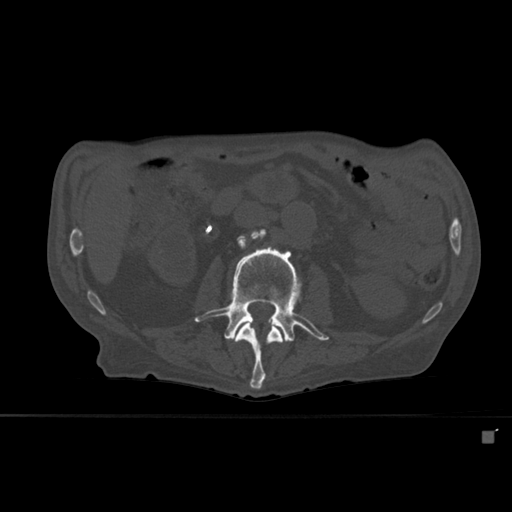
CT including the spine, one axial slice. Slice 220 of 527 in the series (ordered by position). Bone window (W 1800 / L 400 HU). 512 × 512 image matrix, field of view 373 × 373 mm. Male patient, age 78 years. Case-level facts recorded for this patient, not image findings: primary cancer: prostate.
Structures marked on this image (semi-automatic segmentation, software-assisted and operator-edited):
- L2 vertebra: bounding box [x1, y1, x2, y2] px = [234, 323, 283, 389]
- L3 vertebra: [195, 229, 329, 342]
- L4 vertebra: [251, 229, 264, 238]